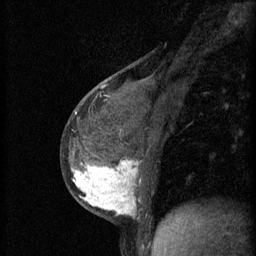
Breast MRI (dynamic contrast-enhanced), one sagittal slice. Slice 27 of 60 in the series (ordered by position). 3 images stored at this slice position (order not interpretable as contrast timing). 1.5 T. TE 4.2 ms, TR 11 ms. 2 mm slice thickness. 256 × 256 image matrix, field of view 180 × 180 mm. Patient: female, 37 years.
Outlined on this slice (semi-automatically segmented with operator editing):
- analysis volume of interest (the breast-tissue region the enhancement analysis was run in; not a lesion): bounding box <65,138,174,221> (left, top, right, bottom; pixels)
- tumour enhancement mask (voxels above the 70 % enhancement threshold inside the analysis volume of interest): <73,160,141,217>